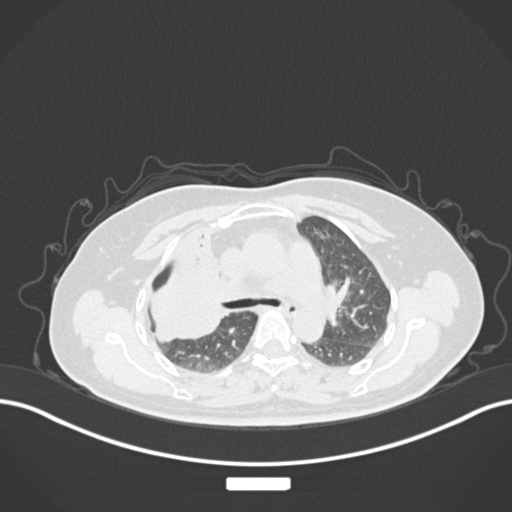
Chest CT, one axial slice; slice 101 of 177 in the series (ordered by position); 120 kVp; lung window (W 1500 / L -600 HU); 1 mm slice thickness; 512 × 512 image matrix, field of view 400 × 400 mm. Patient: female, 60 years. From the clinical record (not read from this slice): clinical TNM (as recorded): T3 N1 M1.
Annotated regions visible in this slice (bounding box drawn by a radiologist):
- lung tumour (recorded histology: adenocarcinoma): bounding box (x1, y1, x2, y2) in pixels: (138, 235, 230, 350)